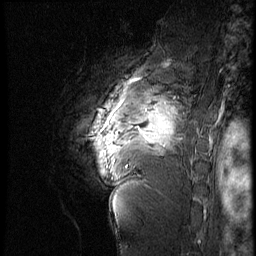
Breast MRI (dynamic contrast-enhanced), one sagittal slice. Slice 51 of 60 in the series (ordered by position). 4 images stored at this slice position (order not interpretable as contrast timing). 1.5 T. TE 4.2 ms, TR 9 ms. 2.5 mm slice thickness. 256 × 256 image matrix. Patient: female, 56 years. Case-level facts recorded for this patient, not image findings: setting: breast cancer imaged before/during neoadjuvant chemotherapy; receptor status: HER2-positive.
Structures marked on this image (semi-automatic segmentation, software-assisted and operator-edited):
- analysis volume of interest (the breast-tissue region the enhancement analysis was run in; not a lesion): box from (x=82, y=83) to (x=199, y=177) px
- tumour enhancement mask (voxels above the 140 % enhancement threshold inside the analysis volume of interest): (x=117, y=104)–(x=177, y=146)